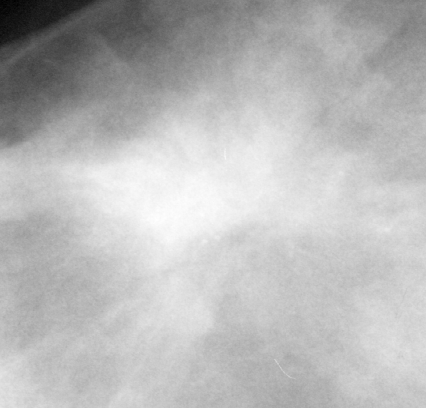
Crop from a digitized film mammogram around one marked abnormality, right breast, CC view.
Finding: mass, shape irregular, margins spiculated; BI-RADS assessment category 5; pathology (as recorded): malignant.